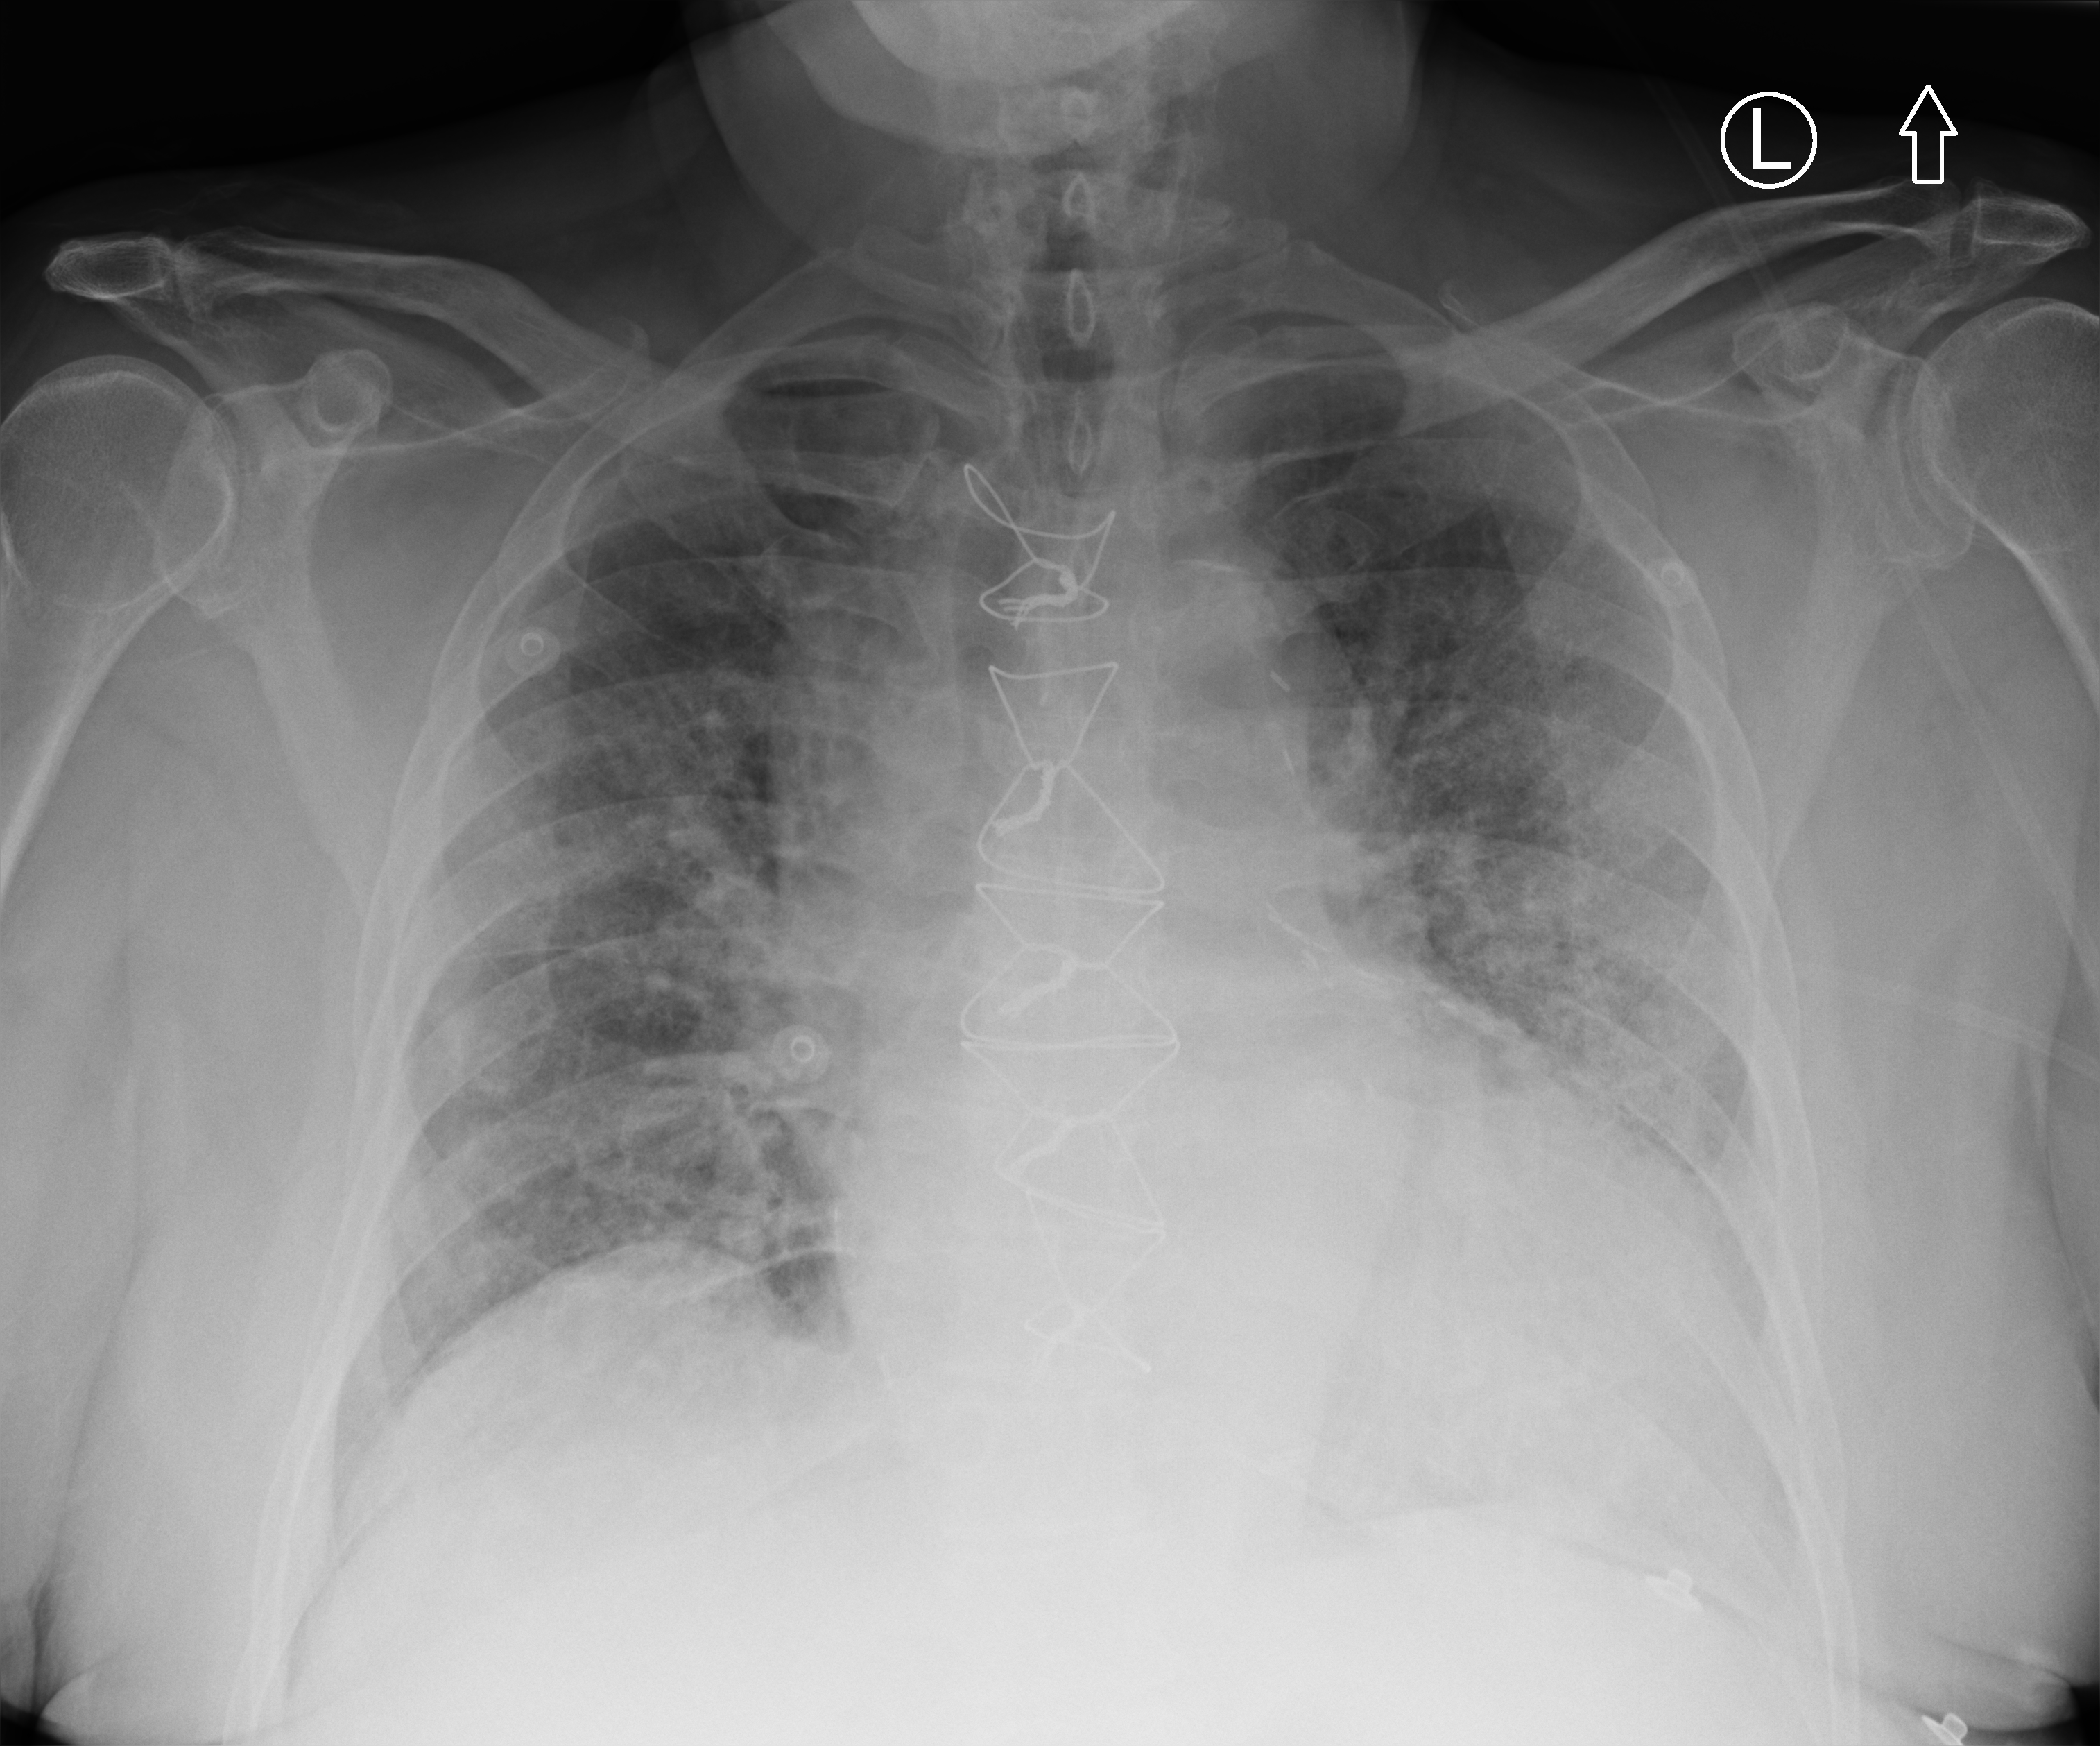
Chest X-ray (portable), anteroposterior (AP) projection. Patient hospitalised with COVID-19; male, aged 75–90 years.
Hospital-stay facts (about this admission, not read from this image; timing relative to this image not recorded):
- COPD (admission record): yes